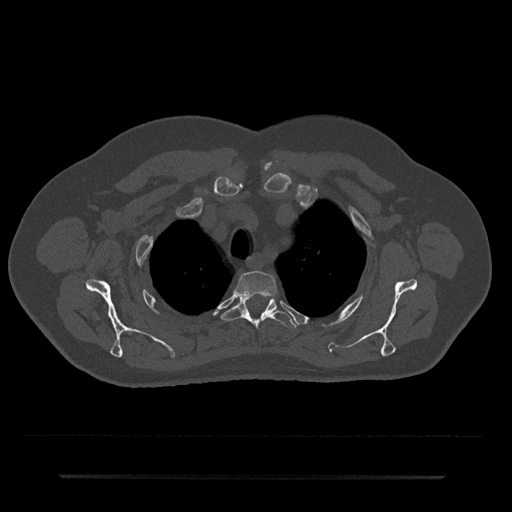
CT including the spine, one axial slice; slice 580 of 797 in the series (ordered by position); reconstruction kernel Br40s/3; bone window (W 1800 / L 400 HU); 512 × 512 image matrix. Male patient, age 69 years. Case-level facts recorded for this patient, not image findings: primary cancer: prostate.
Structures marked on this image (semi-automatically segmented with operator editing):
- T2 vertebra: bounding box <235,271,277,296> (left, top, right, bottom; pixels)
- T3 vertebra: <222,297,297,329>